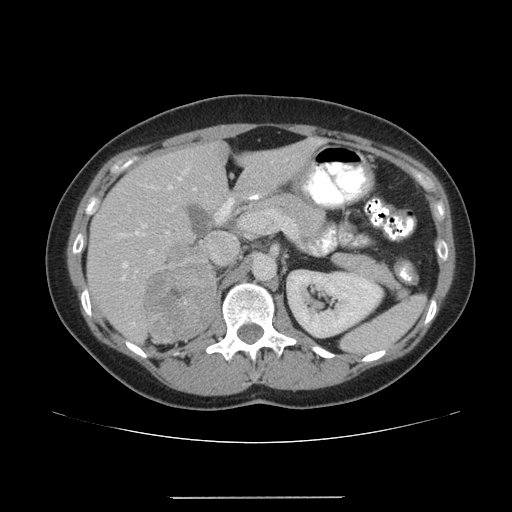
Contrast-enhanced abdominal CT, one axial slice. Slice 107 of 161 in the series (ordered by position). Reconstruction kernel STANDARD. 120 kVp. Intravenous contrast given. Soft-tissue window (W 400 / L 40 HU). 3.75 mm slice thickness. 512 × 512 image matrix, field of view 380 × 380 mm. Female patient. From the clinical record (not read from this slice): diagnosis: adrenocortical carcinoma; tumour side: right adrenal; tumour size at pathology: 9 cm; Ki-67 index: 14 %; stage (as recorded): 3.
Structures marked on this image (semi-automatically segmented with operator editing):
- mass: box from (x=145, y=243) to (x=215, y=343) px